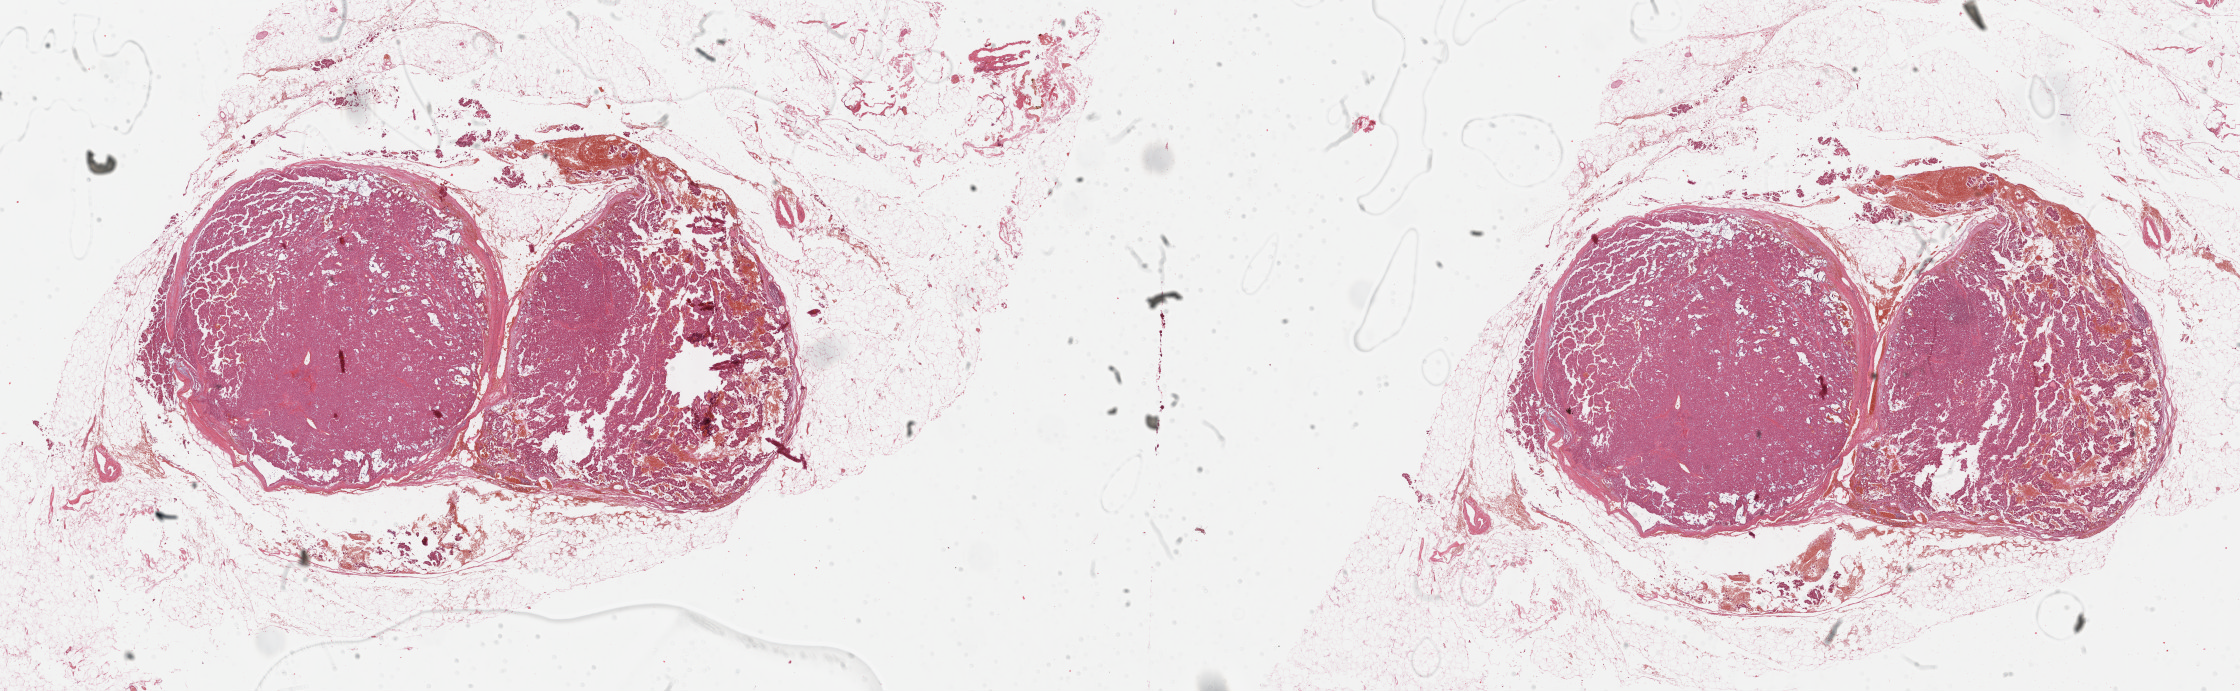
H&E whole-slide image, shown as a low-resolution overview of the whole scanned area (about 36.2 x 11.2 mm, acquisition: 40x scan). Formalin-fixed paraffin-embedded (FFPE) diagnostic section. Adrenal cortex, primary tumour sample. Male patient; age at initial diagnosis 61 years.
Histologic diagnosis: Adrenal cortical carcinoma (cortex of adrenal gland). Lymph nodes positive (case pathology): 6 of 8 examined.